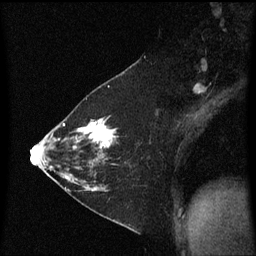
Breast MRI (dynamic contrast-enhanced), one sagittal slice; position 36 of 60 along the scan axis; dynamic contrast-enhanced series, image 2 of 3 at this slice position (ordered by acquisition); 1.5 T; TE 4.2 ms, TR 8.4 ms; 2 mm slice thickness; 256 × 256 image matrix. Female patient, age 36 years. From the clinical record (not read from this slice): setting: breast cancer imaged before/during neoadjuvant chemotherapy; receptor status: HR-positive, HER2-negative.
Outlined on this slice (semi-automatically segmented with operator editing):
- analysis volume of interest (the breast-tissue region the enhancement analysis was run in; not a lesion): bounding box <72,116,119,187> (left, top, right, bottom; pixels)
- tumour enhancement mask (voxels above the 70 % enhancement threshold inside the analysis volume of interest): <74,118,119,151>